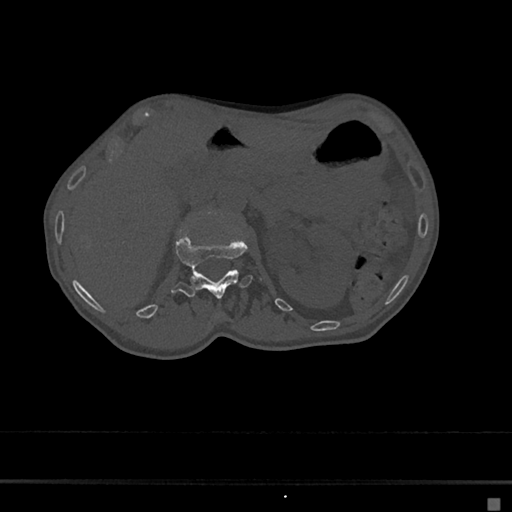
CT including the spine, one axial slice; slice 67 of 797 in the series (ordered by position); reconstruction kernel Br40s/3; 120 kVp; bone window (W 1800 / L 400 HU); 0.5 mm slice thickness; 512 × 512 image matrix, field of view 360 × 360 mm. Patient: female, 68 years. From the clinical record (not read from this slice): primary cancer: renal.
Outlined on this slice (semi-automatic segmentation, software-assisted and operator-edited):
- L1 vertebra: bounding box <171,231,263,298> (left, top, right, bottom; pixels)